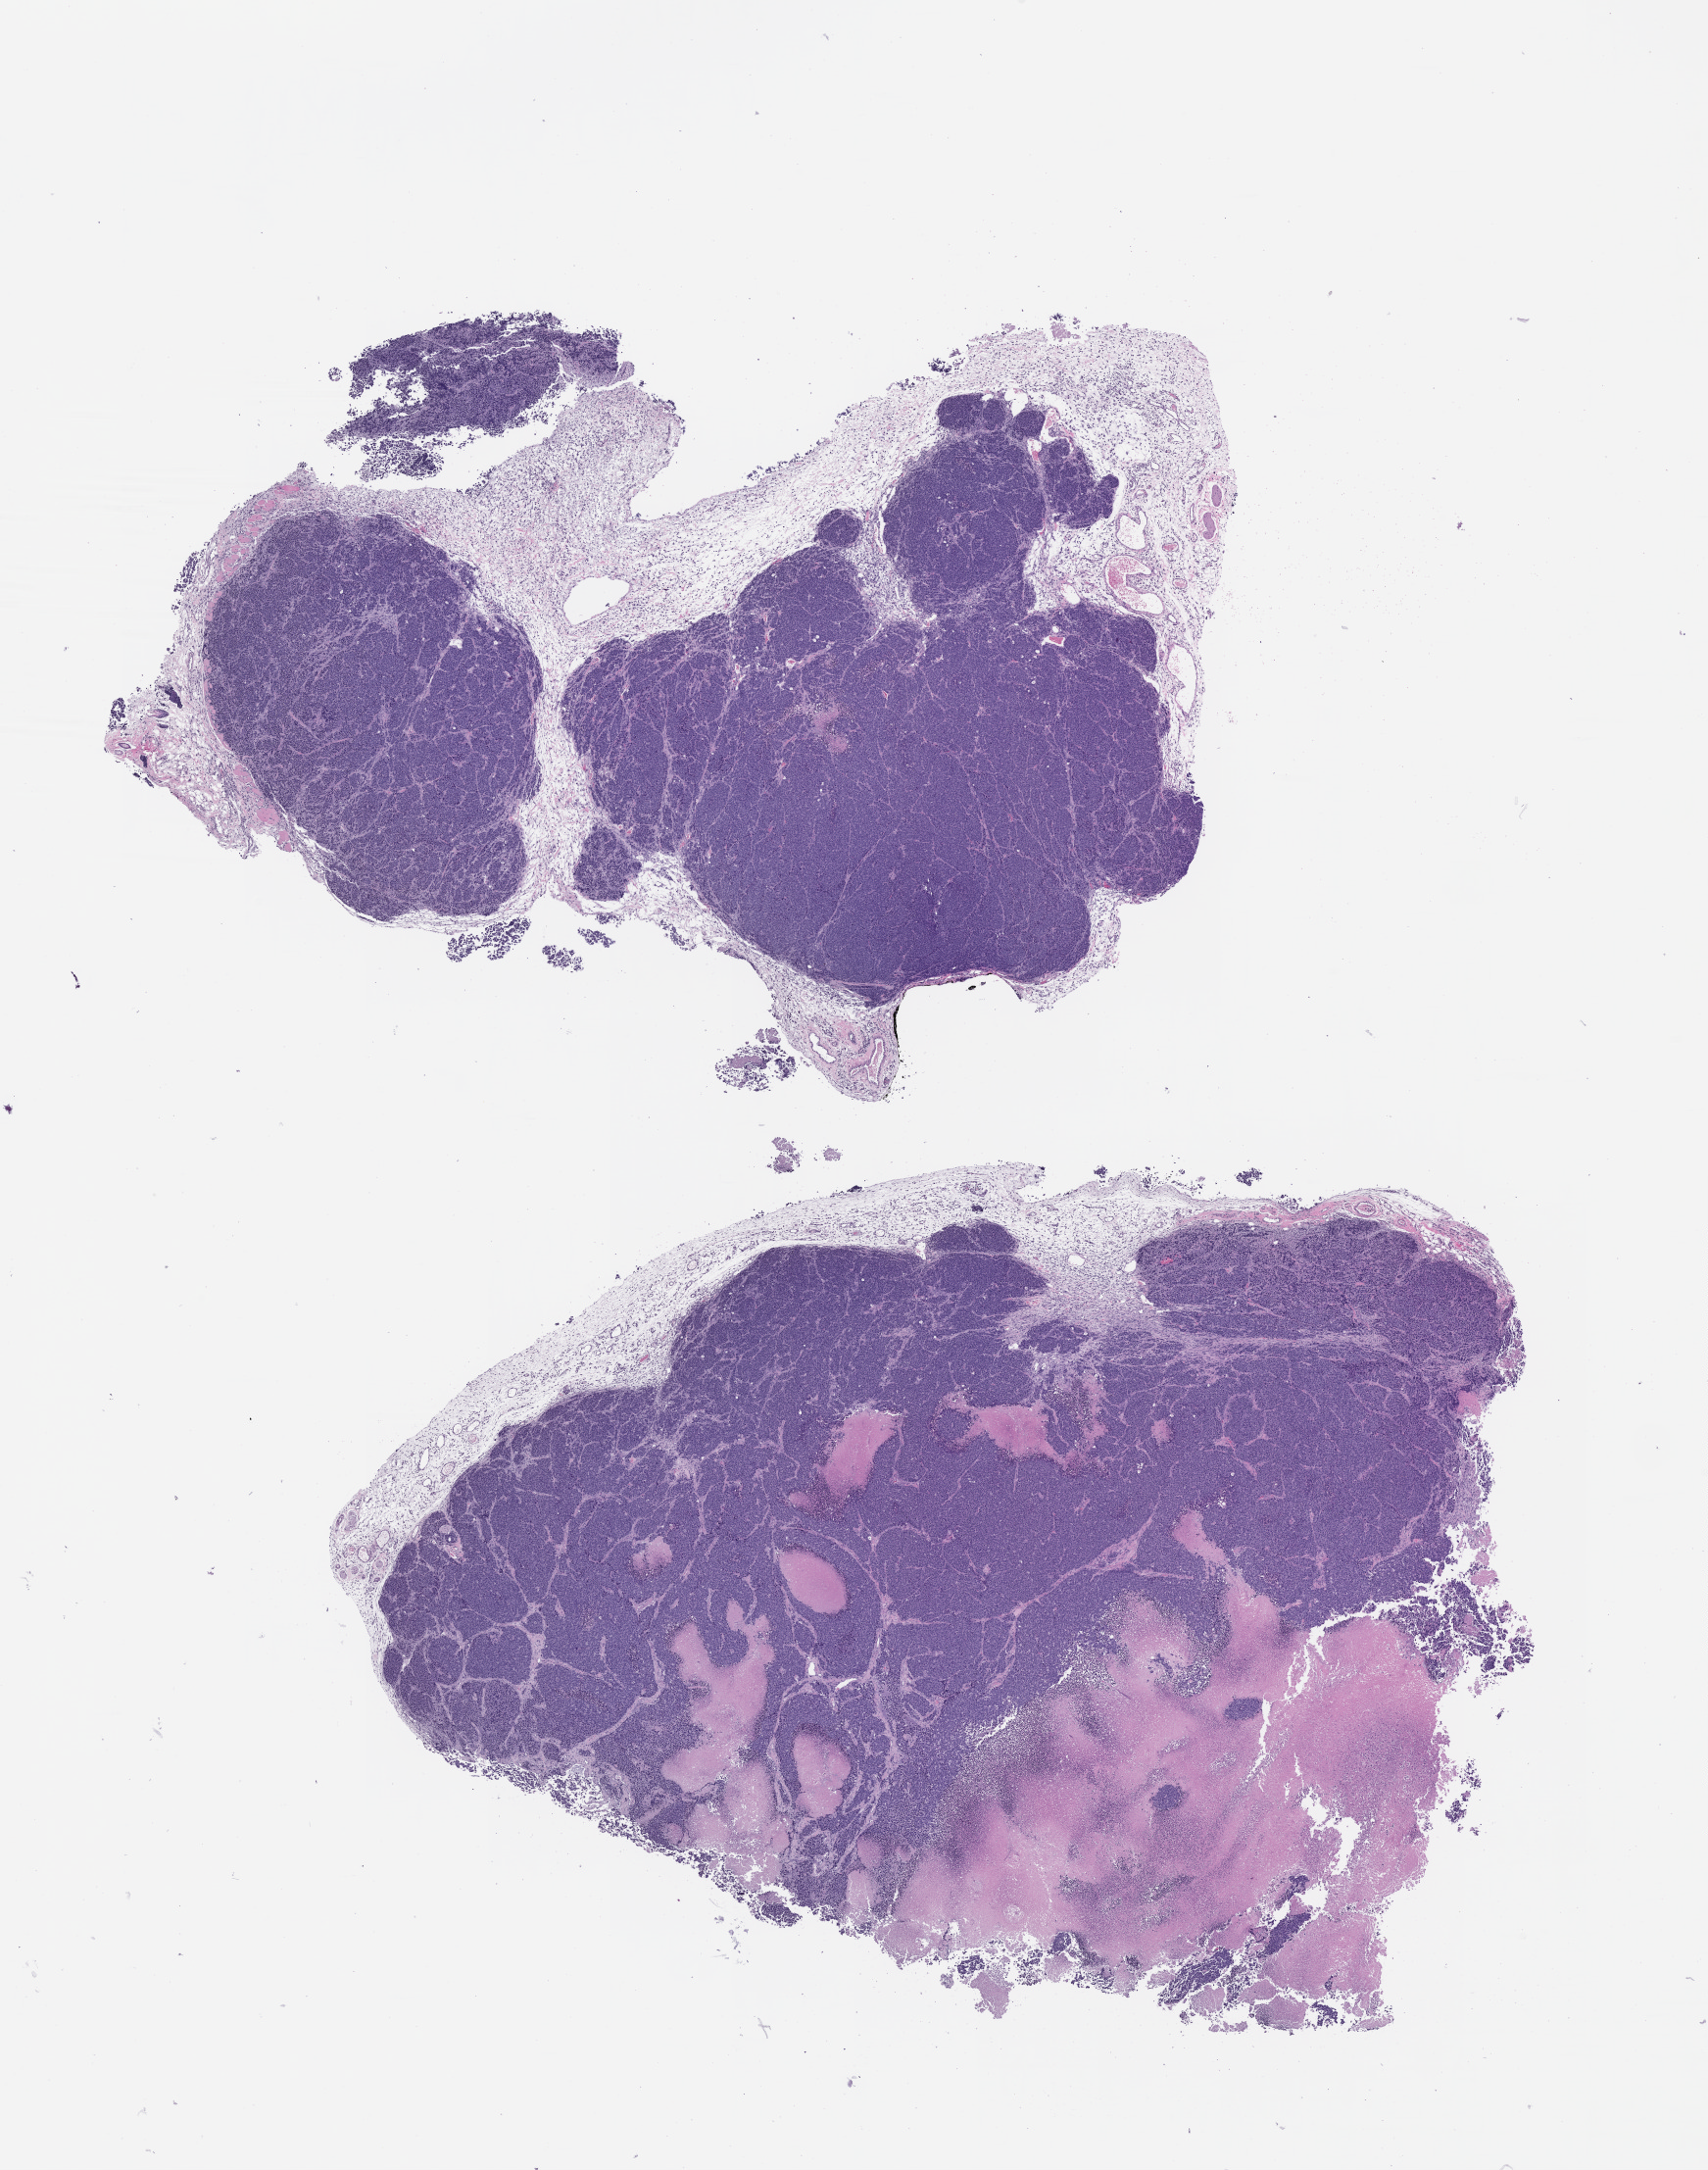
Haematoxylin and eosin whole-slide image of a patient-derived xenograft (PDX) tumor grown in a mouse, passage 1 — low-resolution overview of the scanned area, about 14.0 x 17.8 mm, formalin-fixed paraffin-embedded section, tumor site category: neuroendocrine system.
* originating patient diagnosis: Neuroendocrine Carcinoma